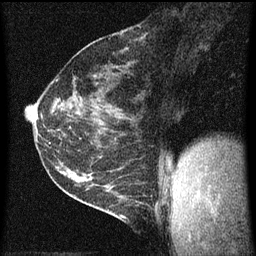
Breast MRI (dynamic contrast-enhanced), one sagittal slice; position 26 of 60 along the scan axis; dynamic contrast-enhanced series, image 2 of 3 at this slice position (ordered by acquisition); 1.5 T; TE 4.2 ms, TR 8 ms; 2 mm slice thickness; 256 × 256 image matrix, field of view 180 × 180 mm. Patient: female, 35 years.
Annotated regions visible in this slice (semi-automatically segmented with operator editing):
- analysis volume of interest (the breast-tissue region the enhancement analysis was run in; not a lesion): bounding box [x1, y1, x2, y2] px = [106, 182, 147, 223]
- tumour enhancement mask (voxels above the 70 % enhancement threshold inside the analysis volume of interest): [120, 200, 127, 219]